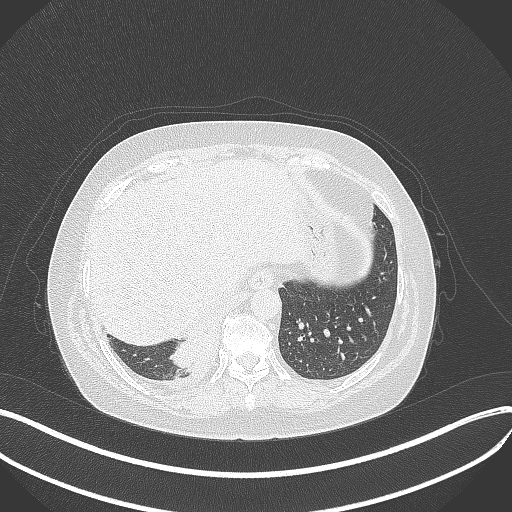
Chest CT, one axial slice; position 82 of 381 along the scan axis; reconstruction kernel B70f; lung window (W 1500 / L -600 HU); 1 mm slice thickness; 512 × 512 image matrix, field of view 400 × 400 mm. Female patient, age 56 years. Case-level facts recorded for this patient, not image findings: clinical TNM (as recorded): T2b N1 M0.
Outlined on this slice (bounding box drawn by a radiologist):
- lung tumour (recorded histology: small cell carcinoma): bounding box <173,332,223,377> (left, top, right, bottom; pixels)